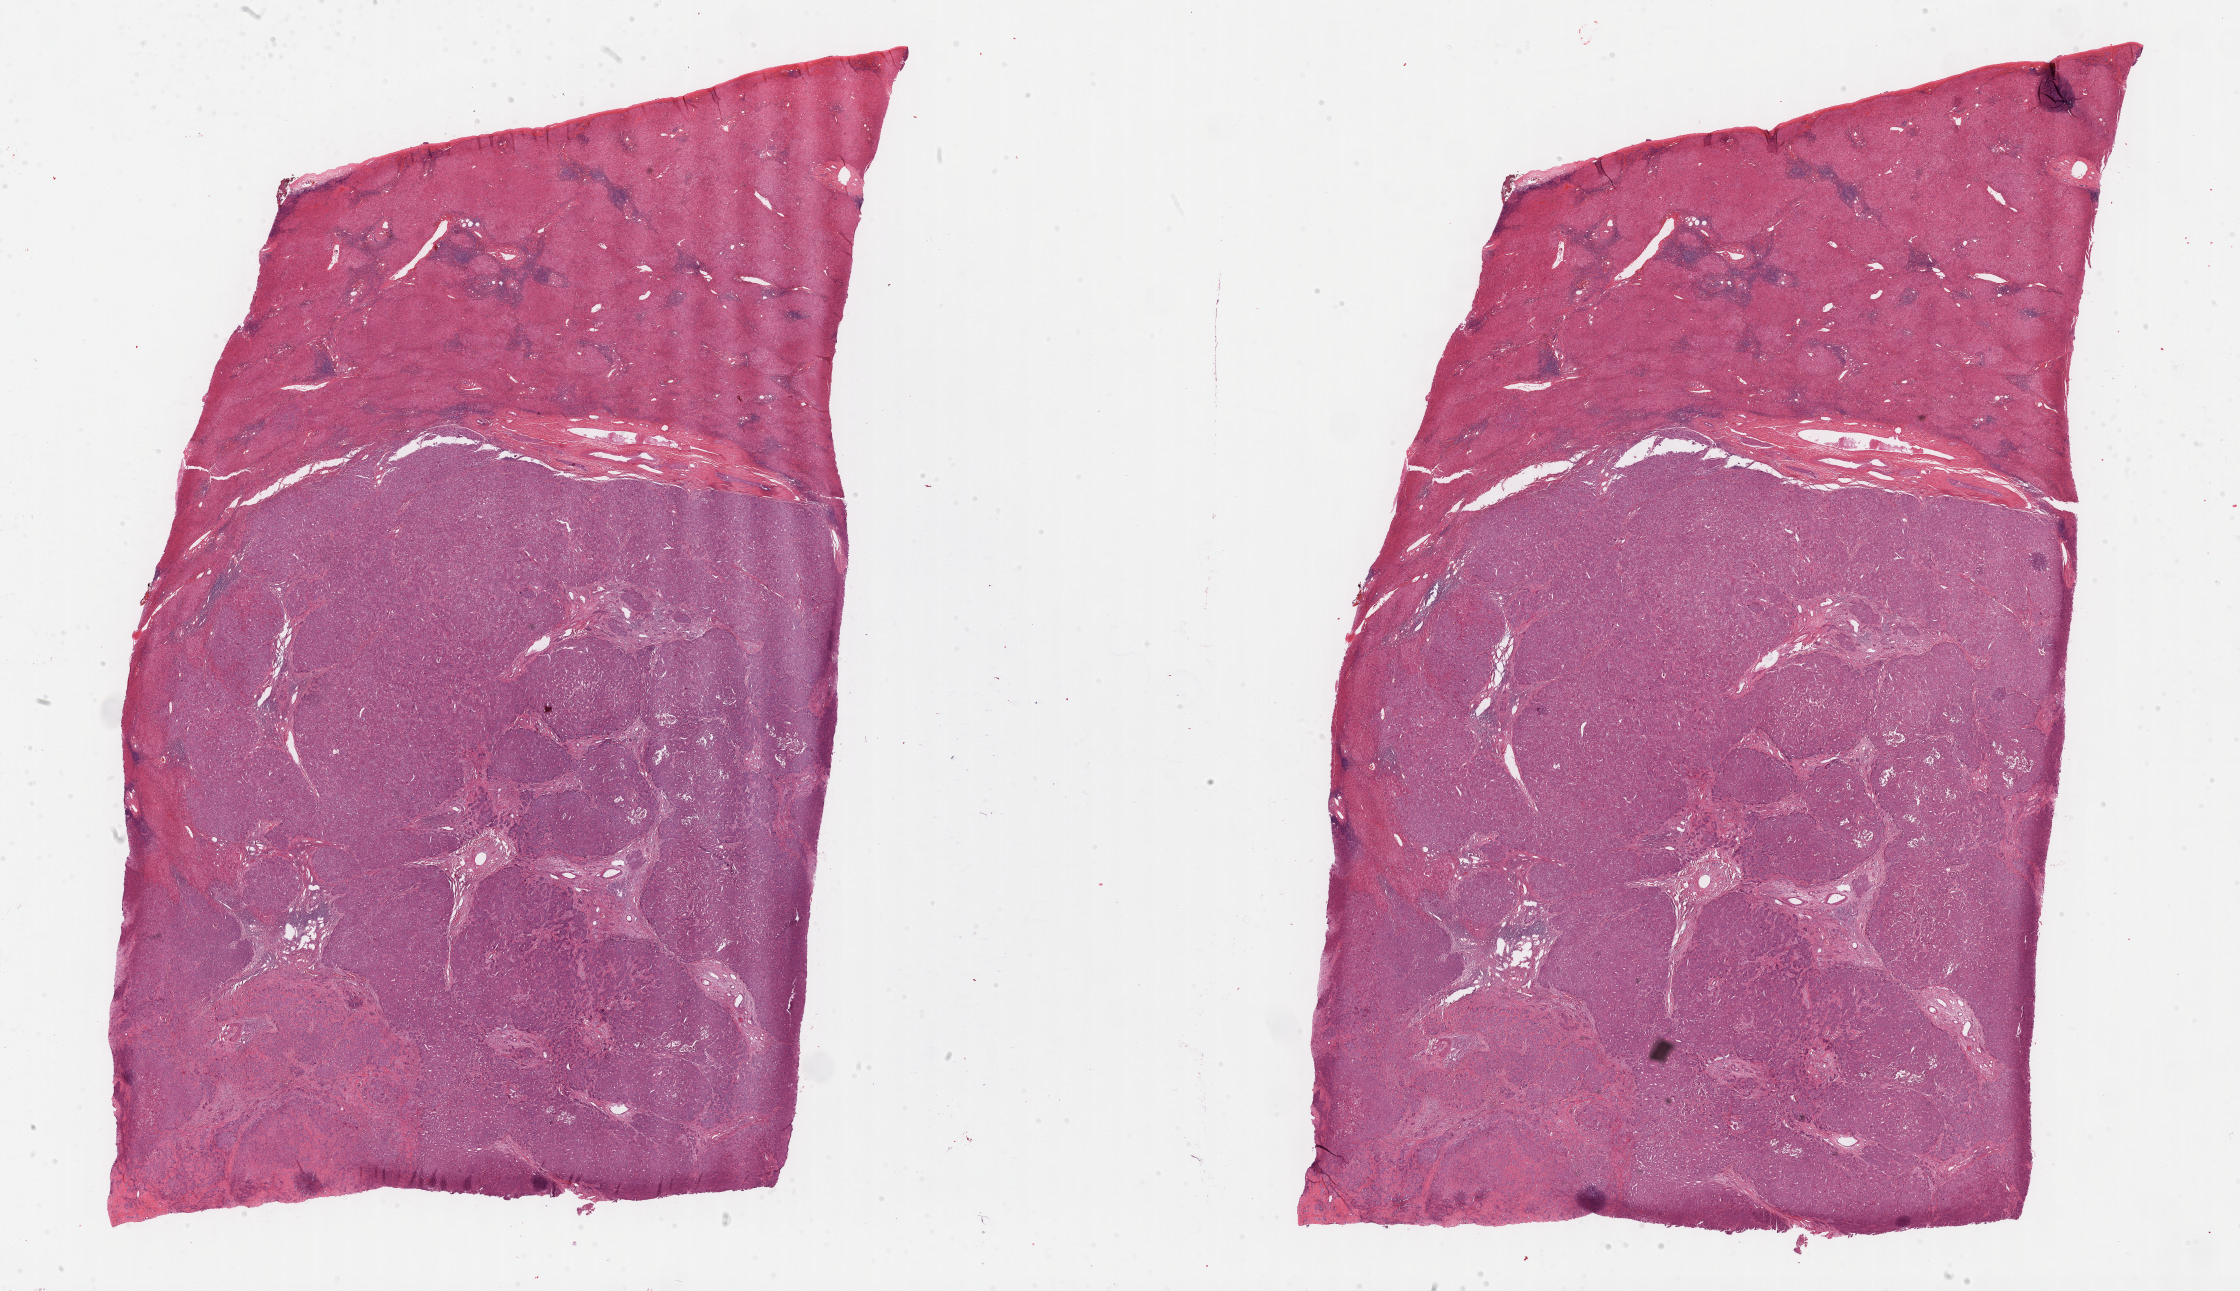
Digitized H&E tissue section (whole slide), shown as a low-resolution overview of the whole scanned area (about 36.2 x 20.9 mm), FFPE section, primary tumour sample from the liver. Male, age 51 years at initial diagnosis. Histologic grade: G2 (moderately differentiated).
Pathologic diagnosis: Hepatocellular carcinoma, NOS.